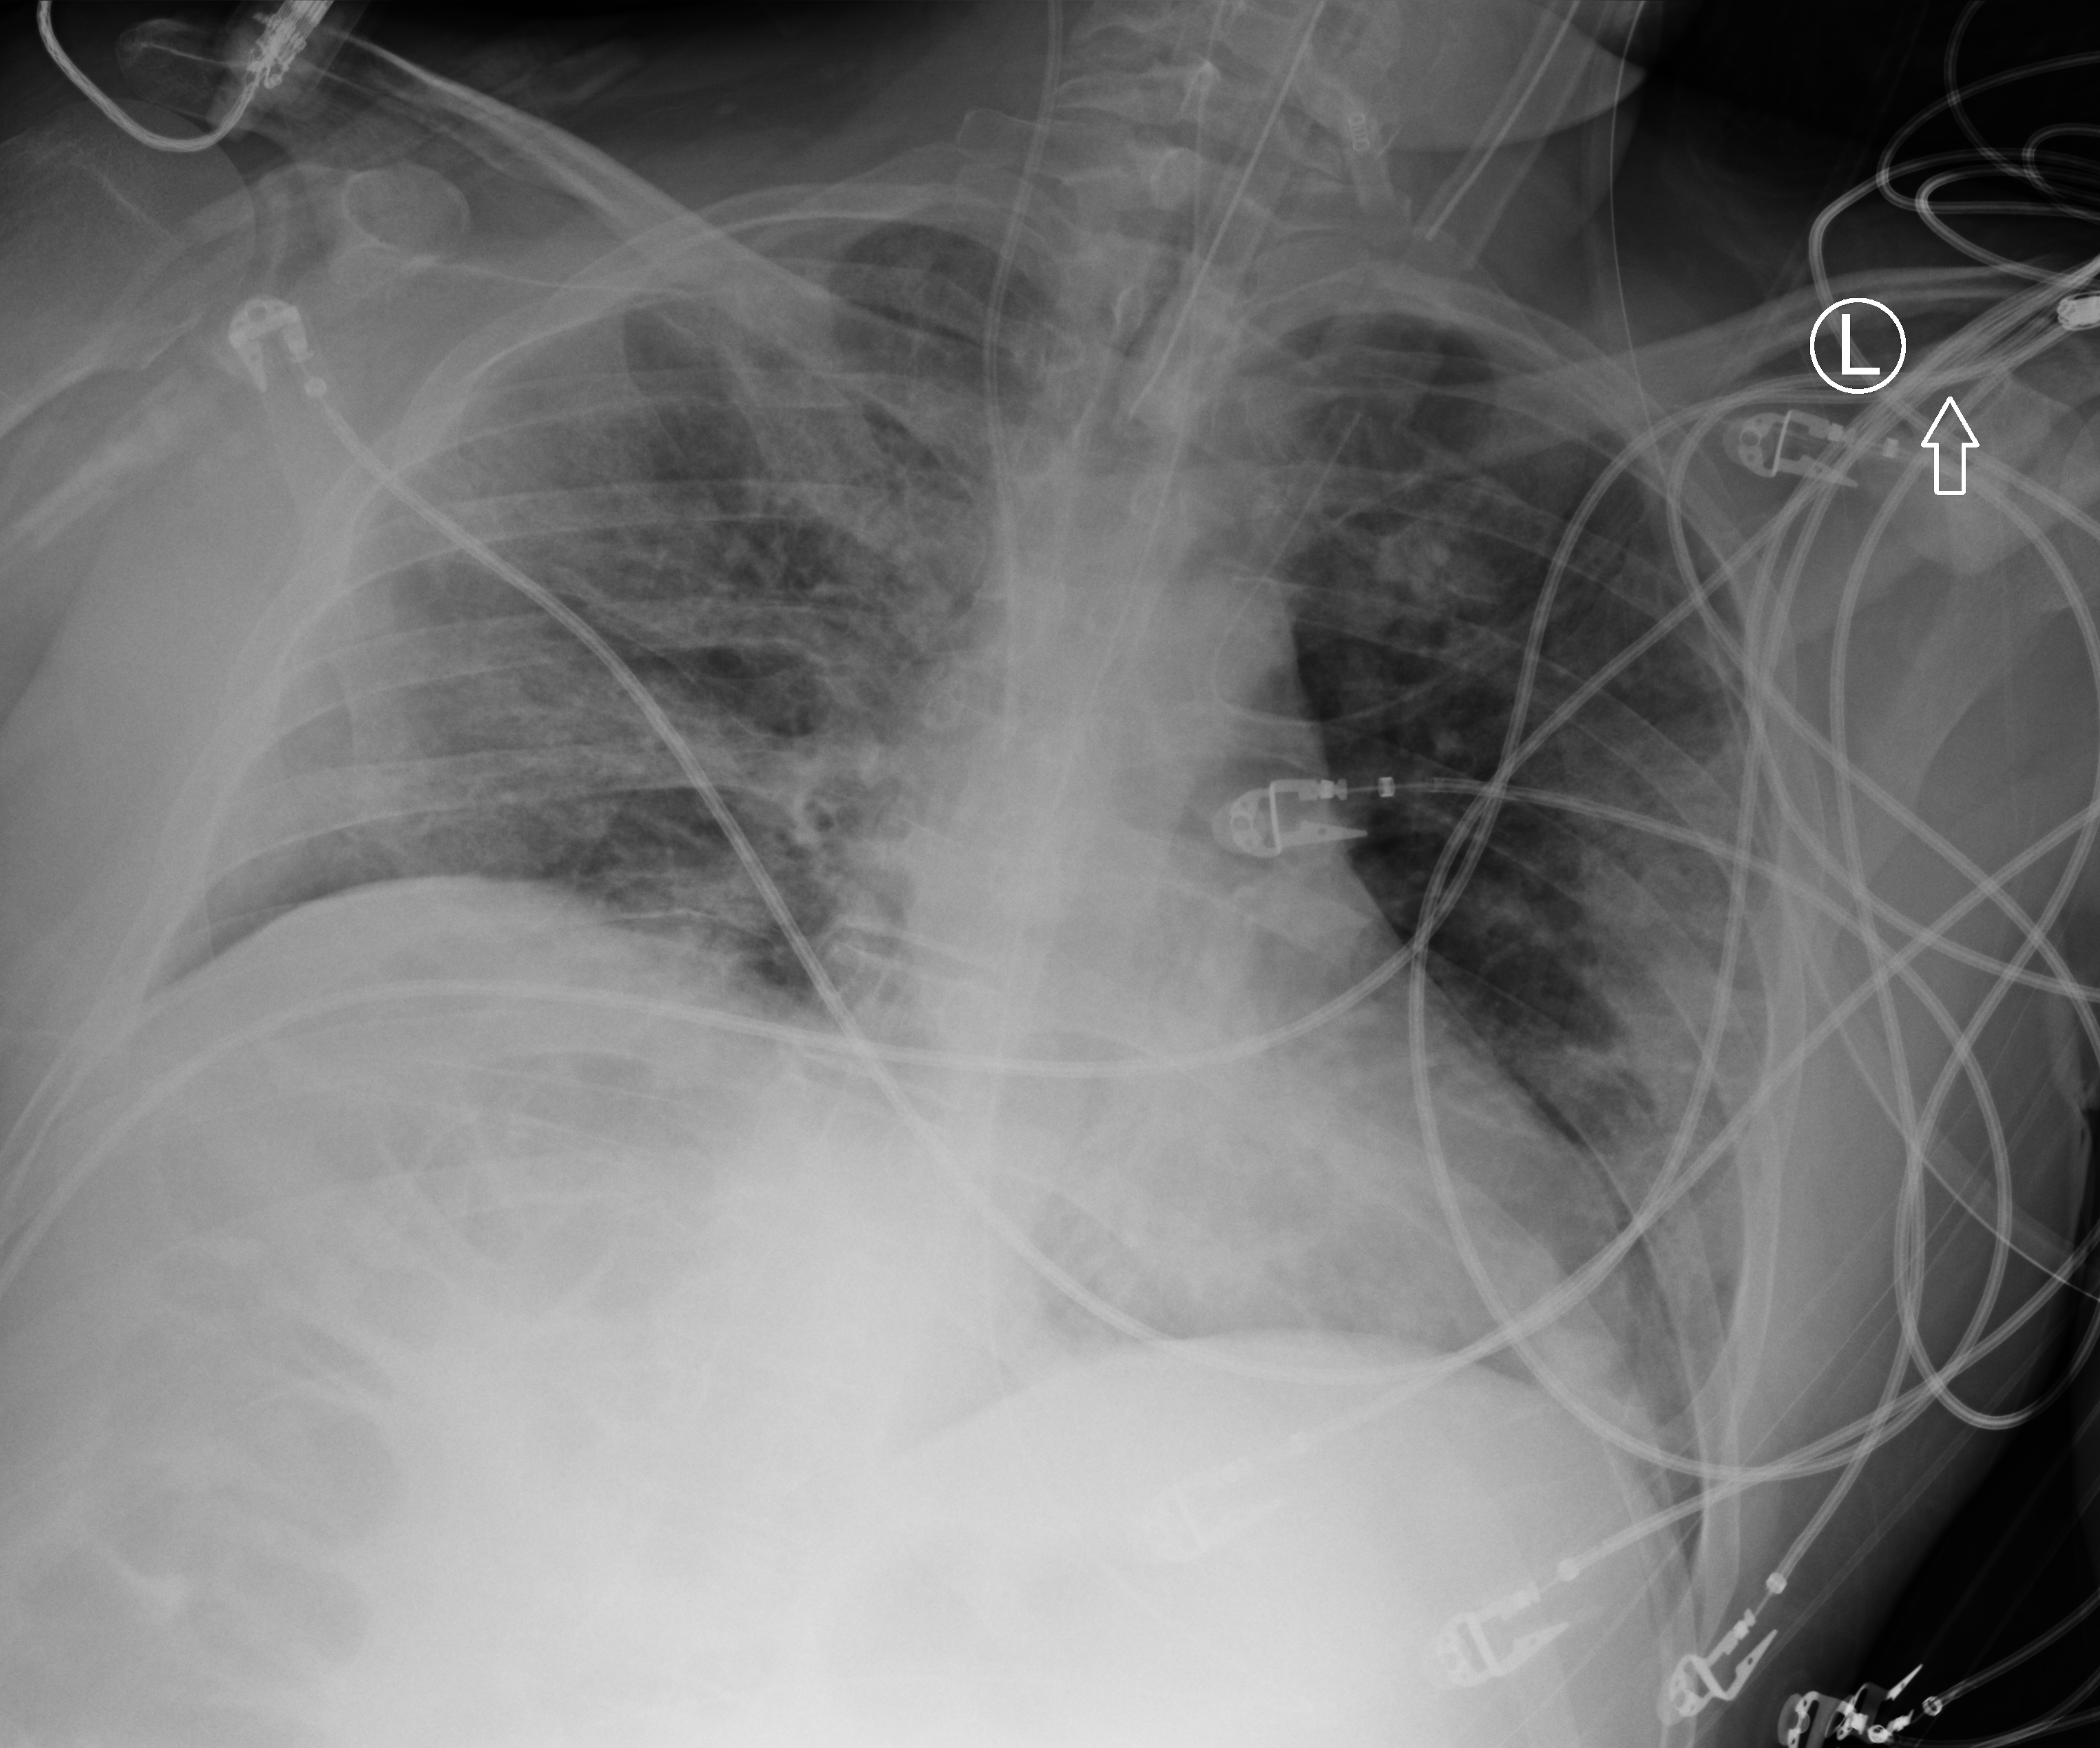
Portable chest radiograph; anteroposterior (AP) projection. Patient hospitalised with COVID-19; male, aged 18–59 years.
From the hospital-stay record, not from the radiograph (when in the stay this image was taken is not recorded): chronic kidney disease (admission record): no.